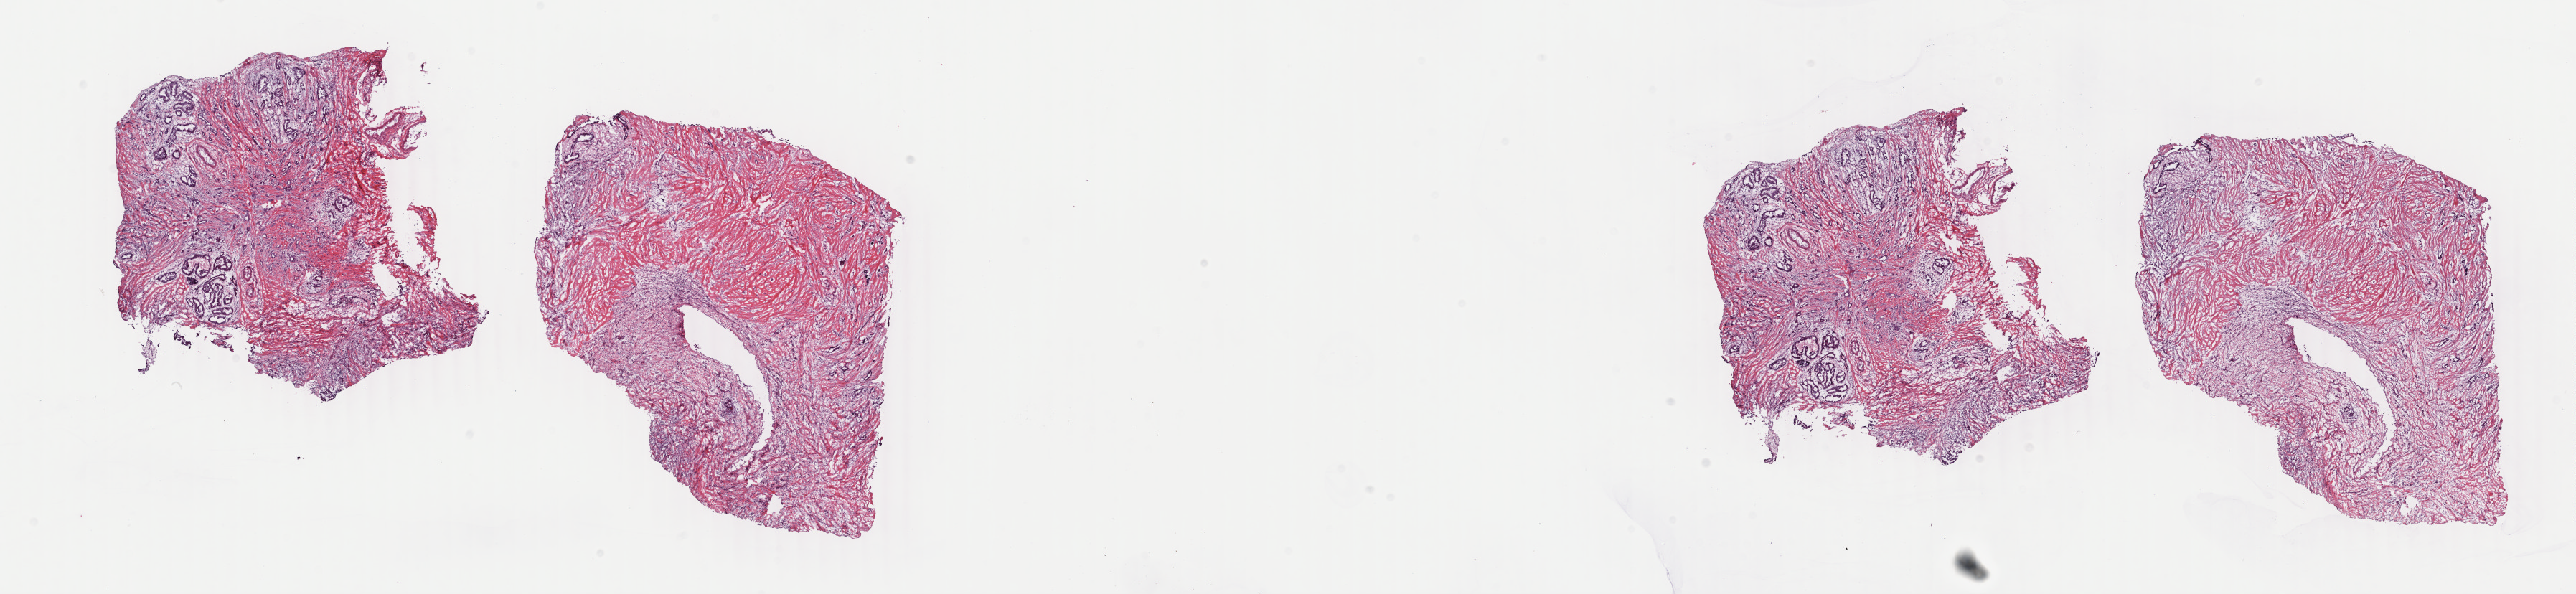
Digitized H&E-stained tissue section (whole slide), low-resolution overview of the scanned area, about 28.6 x 6.6 mm (acquisition: 40x scan). Frozen section. Breast, primary tumour sample. Female, age 47 years at initial diagnosis. Pathologist review of this section (percent, as recorded): tumour cells 70%, tumour nuclei 70%.
Diagnosis: Infiltrating duct carcinoma, NOS.